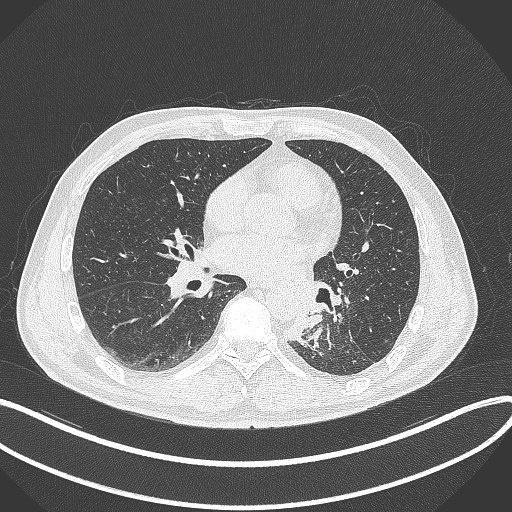
Chest CT, one axial slice. Position 149 of 329 along the scan axis. Reconstruction kernel B70f. 120 kVp. Lung window (W 1500 / L -600 HU). 1 mm slice thickness. 512 × 512 image matrix, field of view 400 × 400 mm. Patient: male, 59 years. Case-level facts recorded for this patient, not image findings: clinical TNM (as recorded): T2a N2 M0.
Outlined on this slice (rectangle marked by the reading radiologist):
- lung tumour (recorded histology: squamous cell carcinoma): bounding box [x1, y1, x2, y2] px = [279, 295, 327, 351]